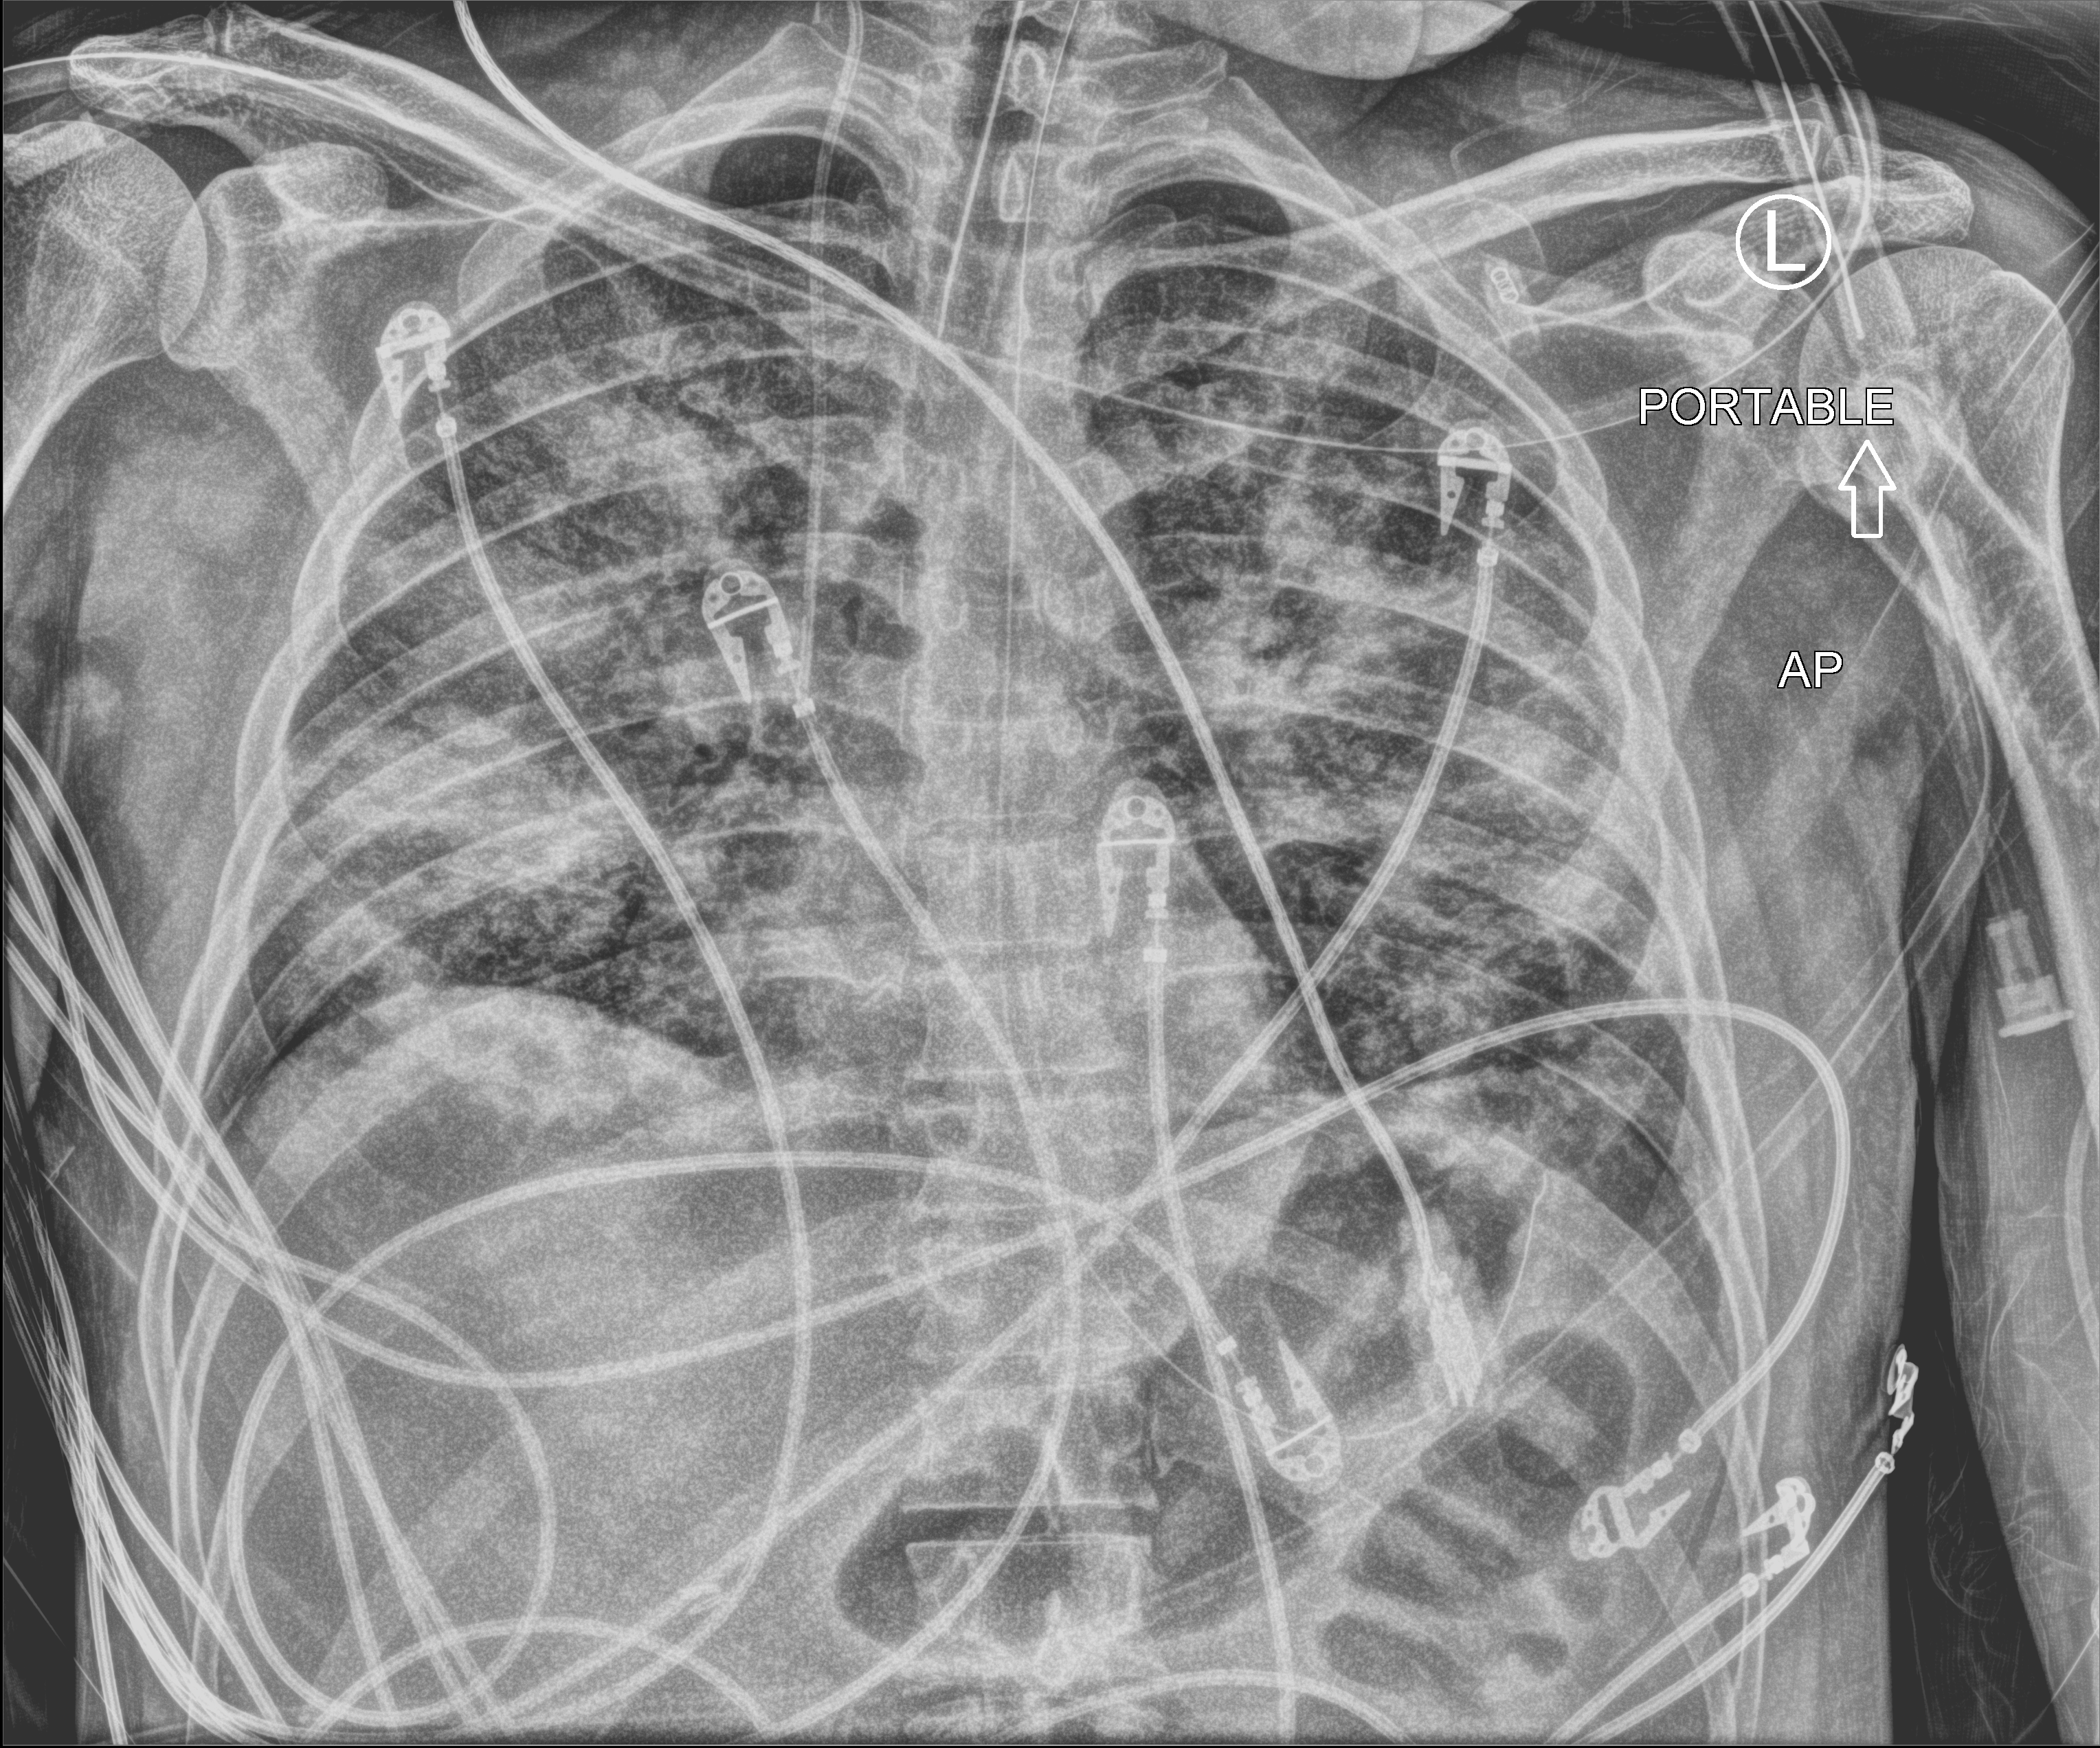
Bedside chest radiograph (computed radiography), anteroposterior (AP) projection. Patient hospitalised with COVID-19; male, aged 18–59 years.
From the hospital-stay record, not from the radiograph (when in the stay this image was taken is not recorded):
- length of hospital stay: 29 days
- mechanically ventilated during this hospital stay: yes